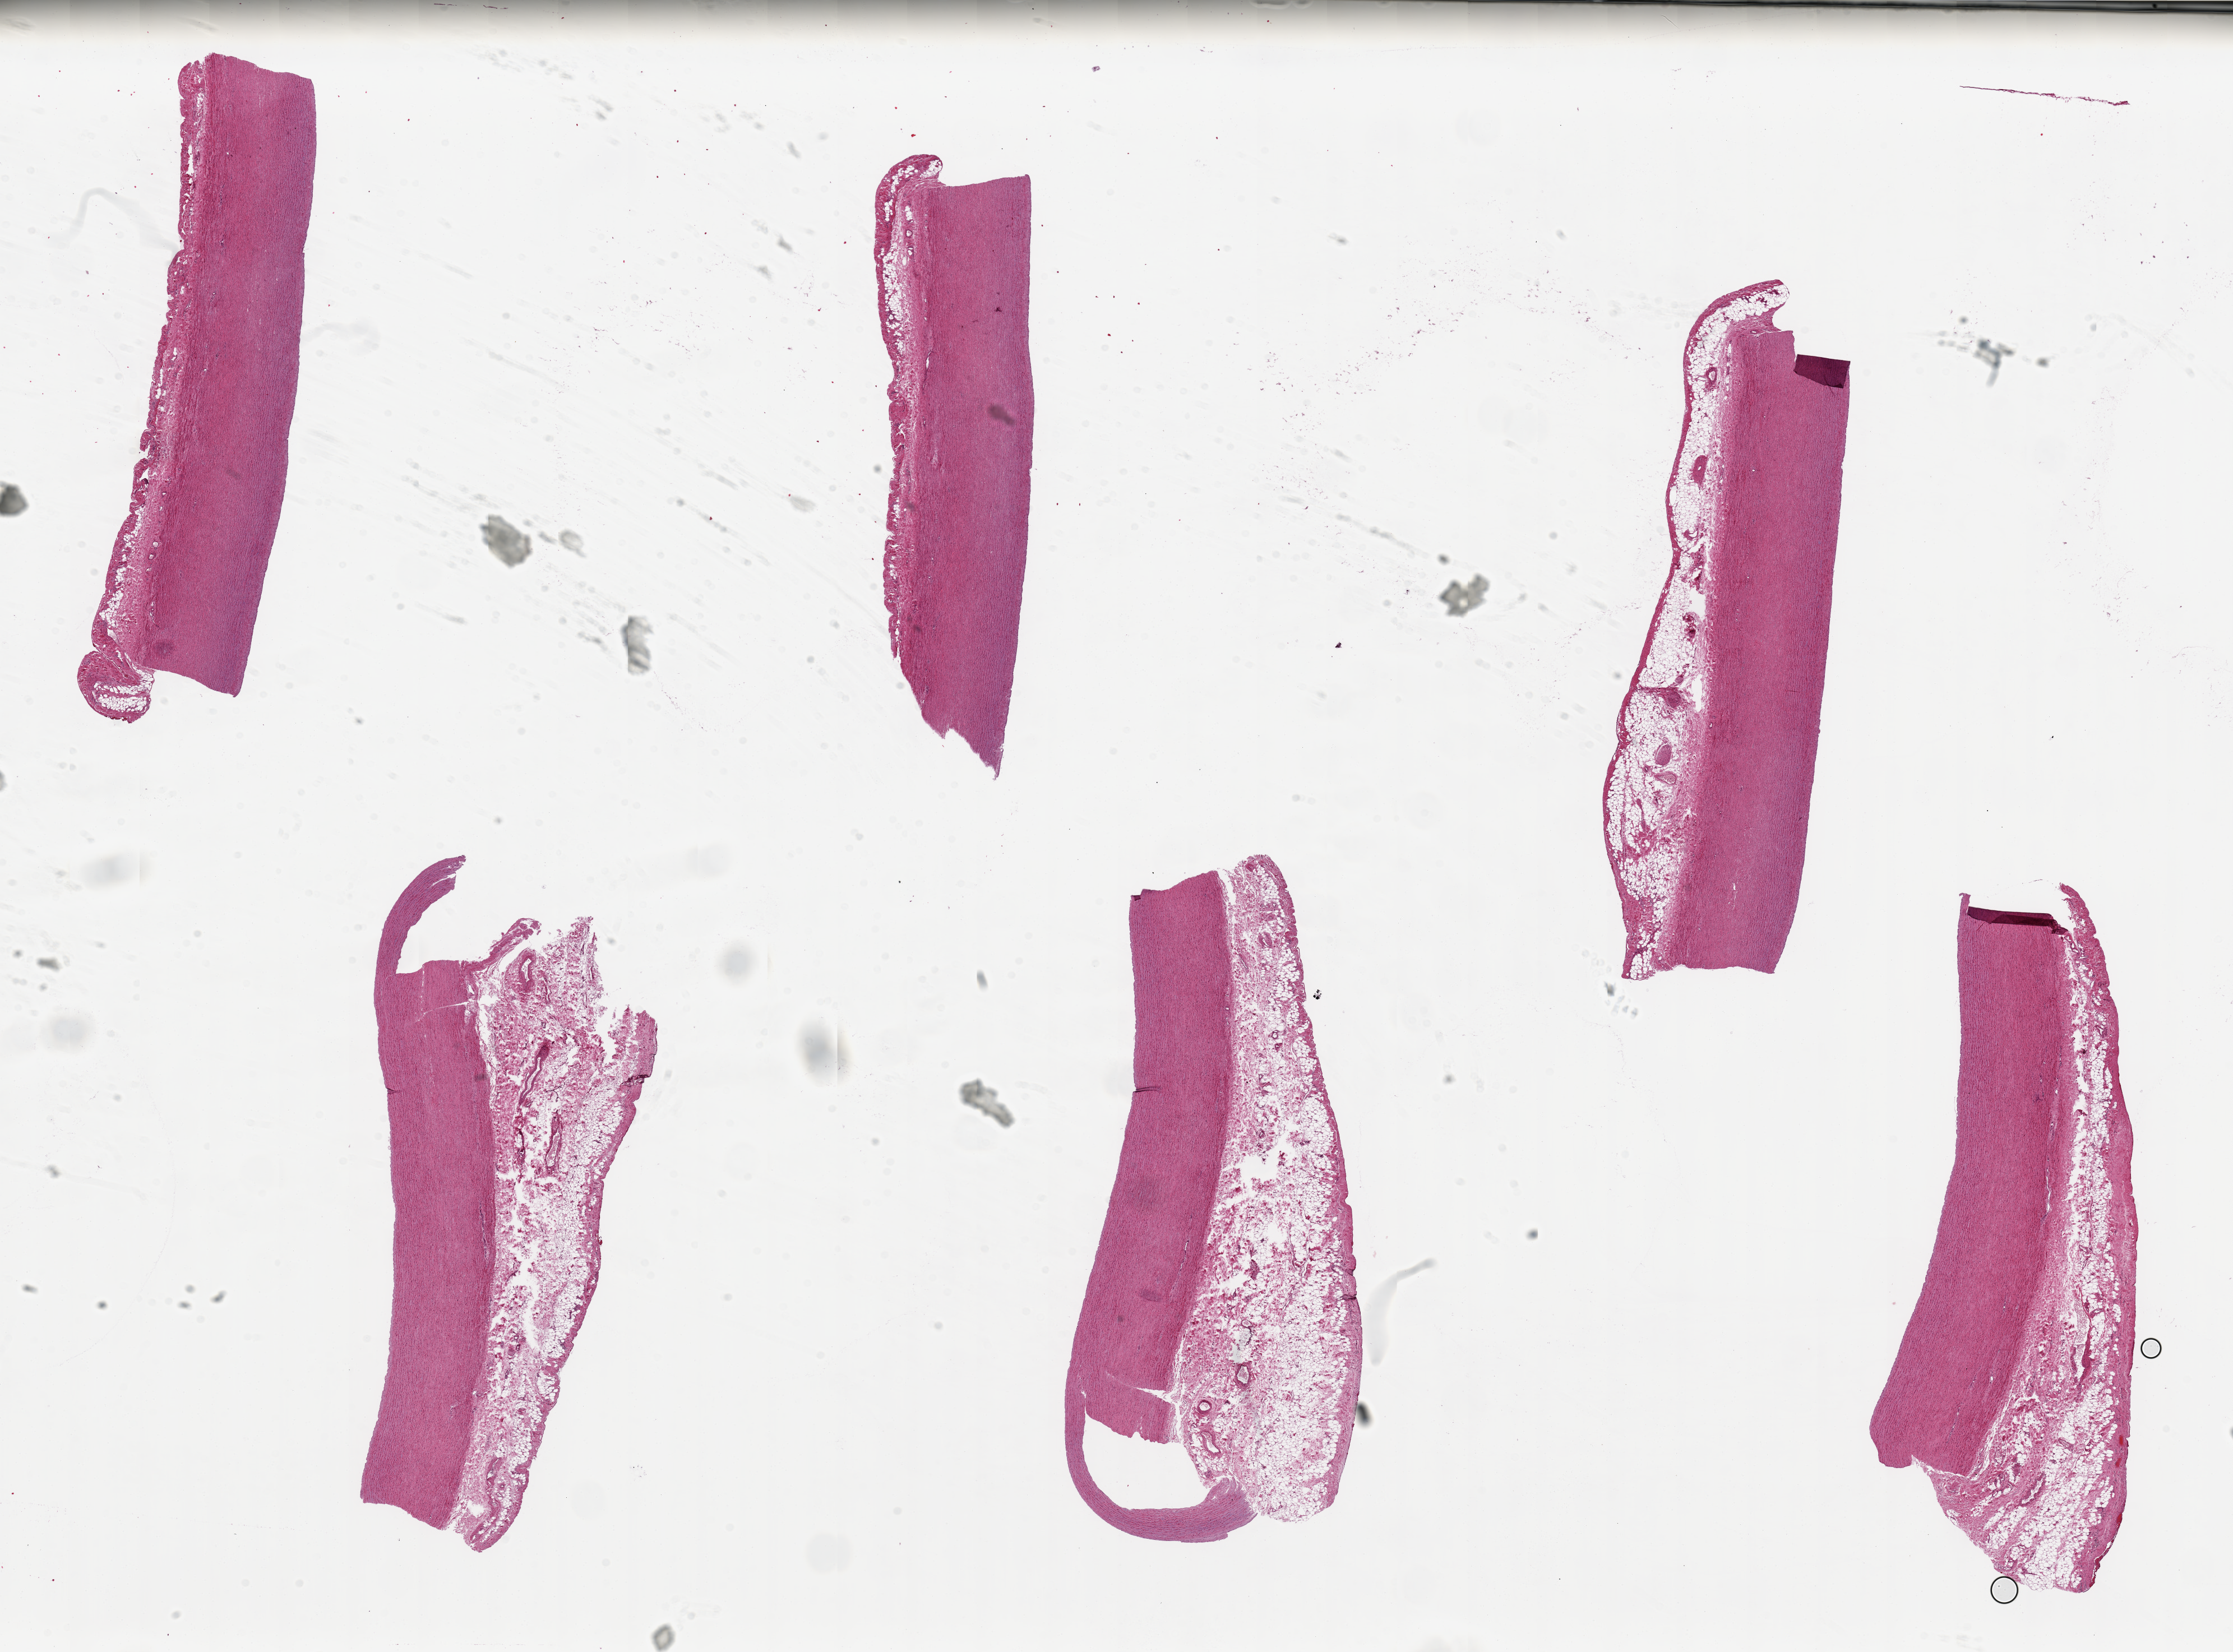
Whole-slide image, haematoxylin and eosin stain, brightfield — whole scanned area (about 31.5 x 23.3 mm) shown as a low-resolution overview; PAXgene-fixed paraffin-embedded (PFPE) section; section of aorta (target tissue); tissue donor sample. Donor sex: male.
Pathologist's review note for this sample: 6 pieces, ~9x2mm, 4 of 6 with adherent fat/vasa vasorum up to 2mm thick.